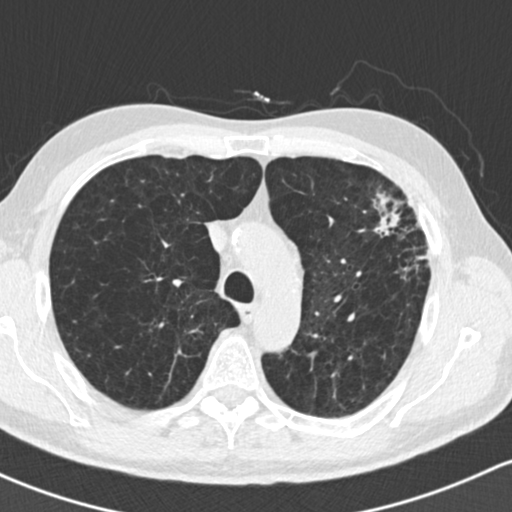
Low-dose screening chest CT, axial slice, first (baseline) screen, lung window (W 1500 / L -600 HU), 2 mm slice thickness, standard (soft-tissue) reconstruction kernel (B30f), 120 kVp, slice 49 of 162 in the series. Male, age 61 years at enrolment. Former smoker at enrolment.
• Expert-annotated lung lesion, box from (x=352, y=183) to (x=443, y=287) px.
• Reader record for this screening exam (exam-level; its link to the box is not recorded): non-calcified nodule or mass ≥4 mm, left upper lobe, 35 × 35 mm, spiculated (stellate) margins, soft tissue attenuation.
• Later outcome: lung cancer diagnosed 19 days after this screen — adenocarcinoma, NOS, left upper lobe, well differentiated (G1), stage IIIA (AJCC 6th edition), 45 mm at pathology.